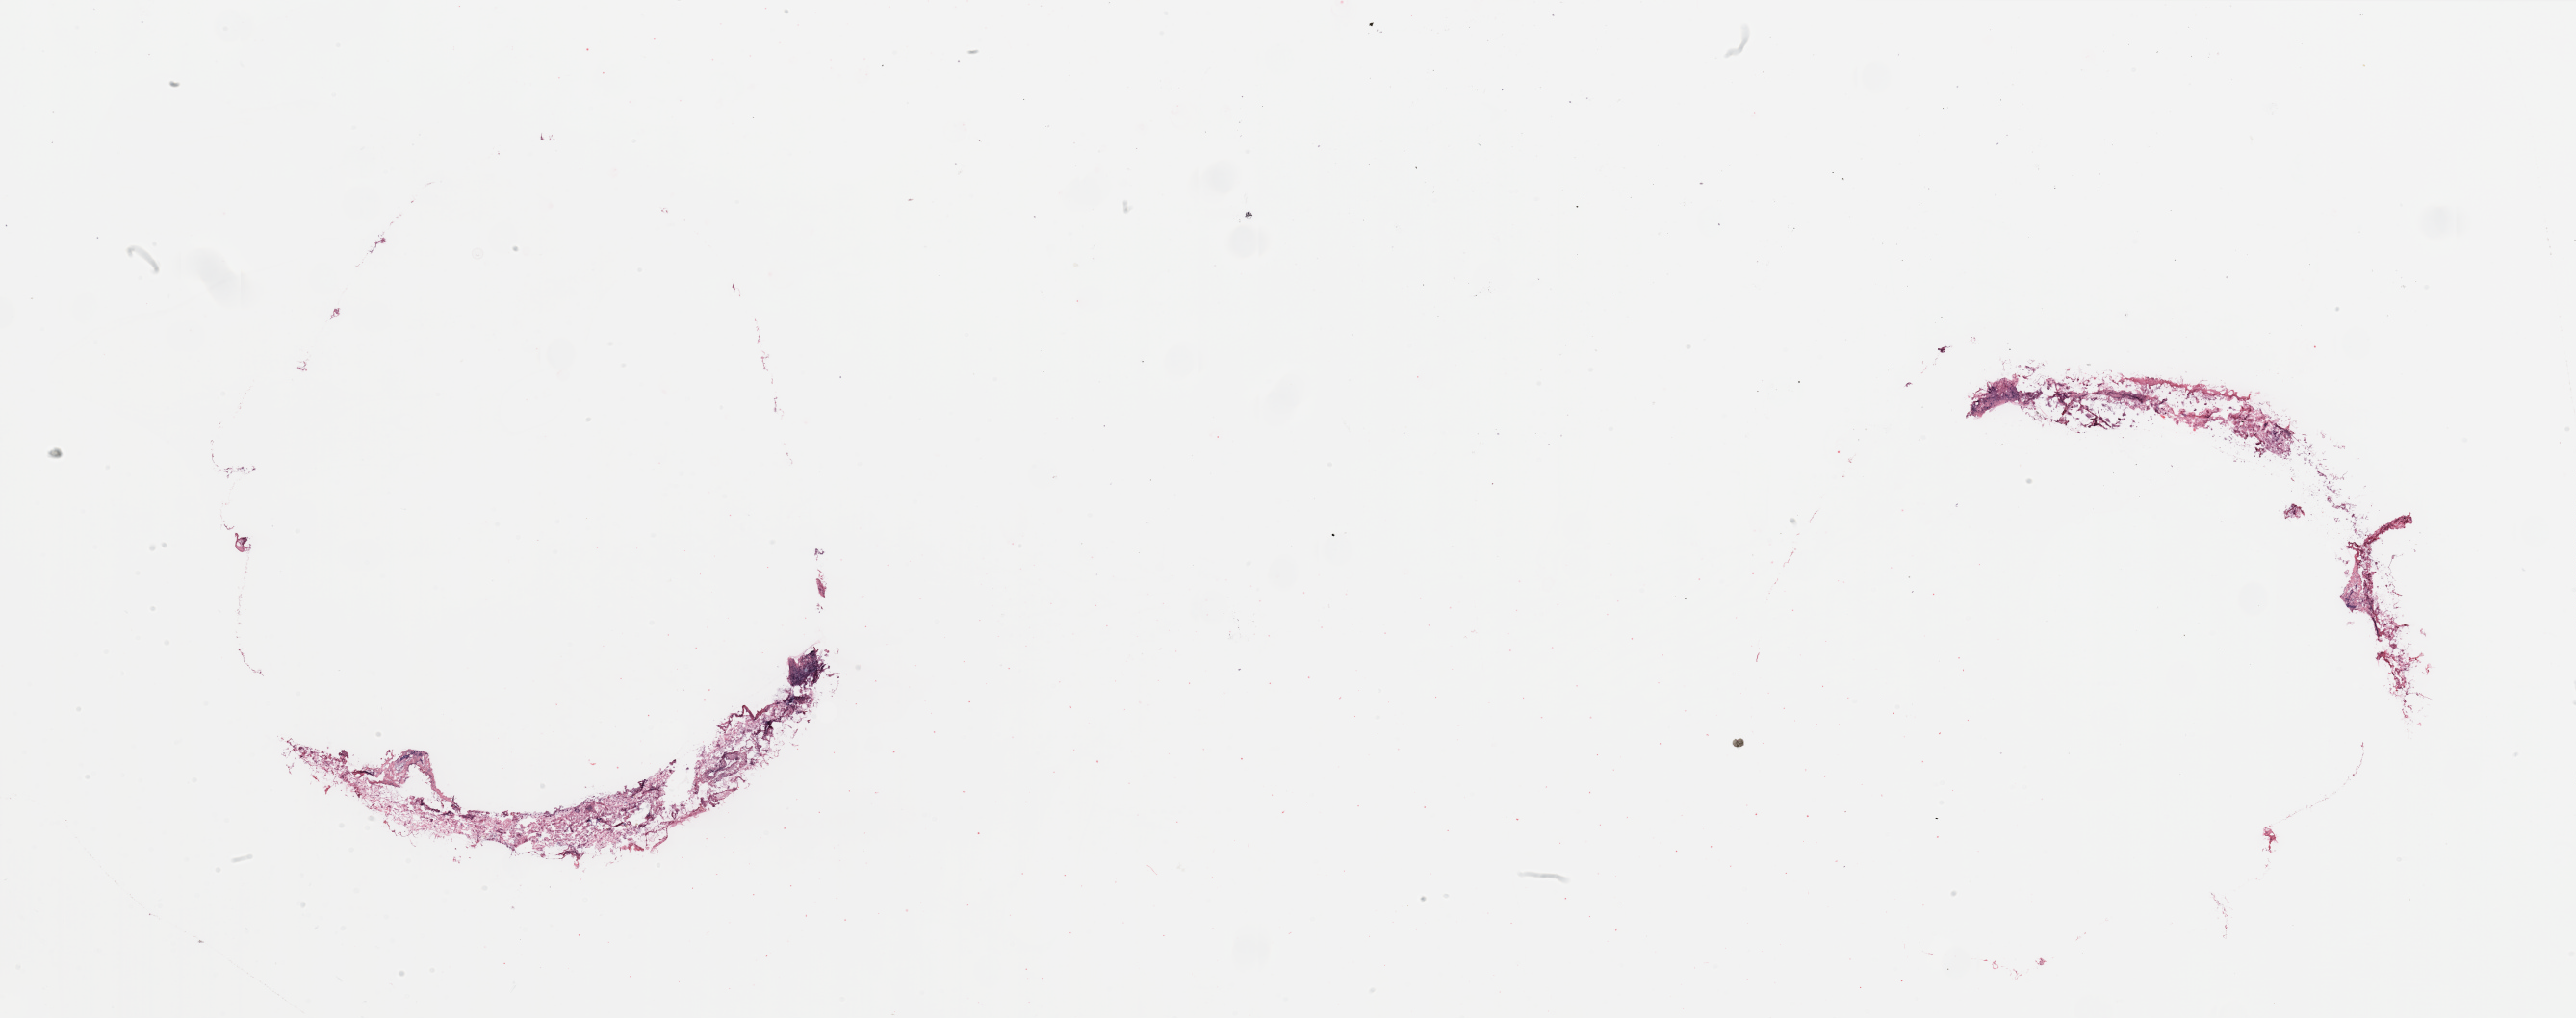
Whole-slide histology image, Hematoxylin and eosin (H&E) stained, whole scanned area (about 42.3 x 16.7 mm) shown as a low-resolution overview, tumour tissue sample, breast. Female, 70 y/o.
* diagnosis: Infiltrating duct carcinoma, NOS
* AJCC pathologic stage: IIIC